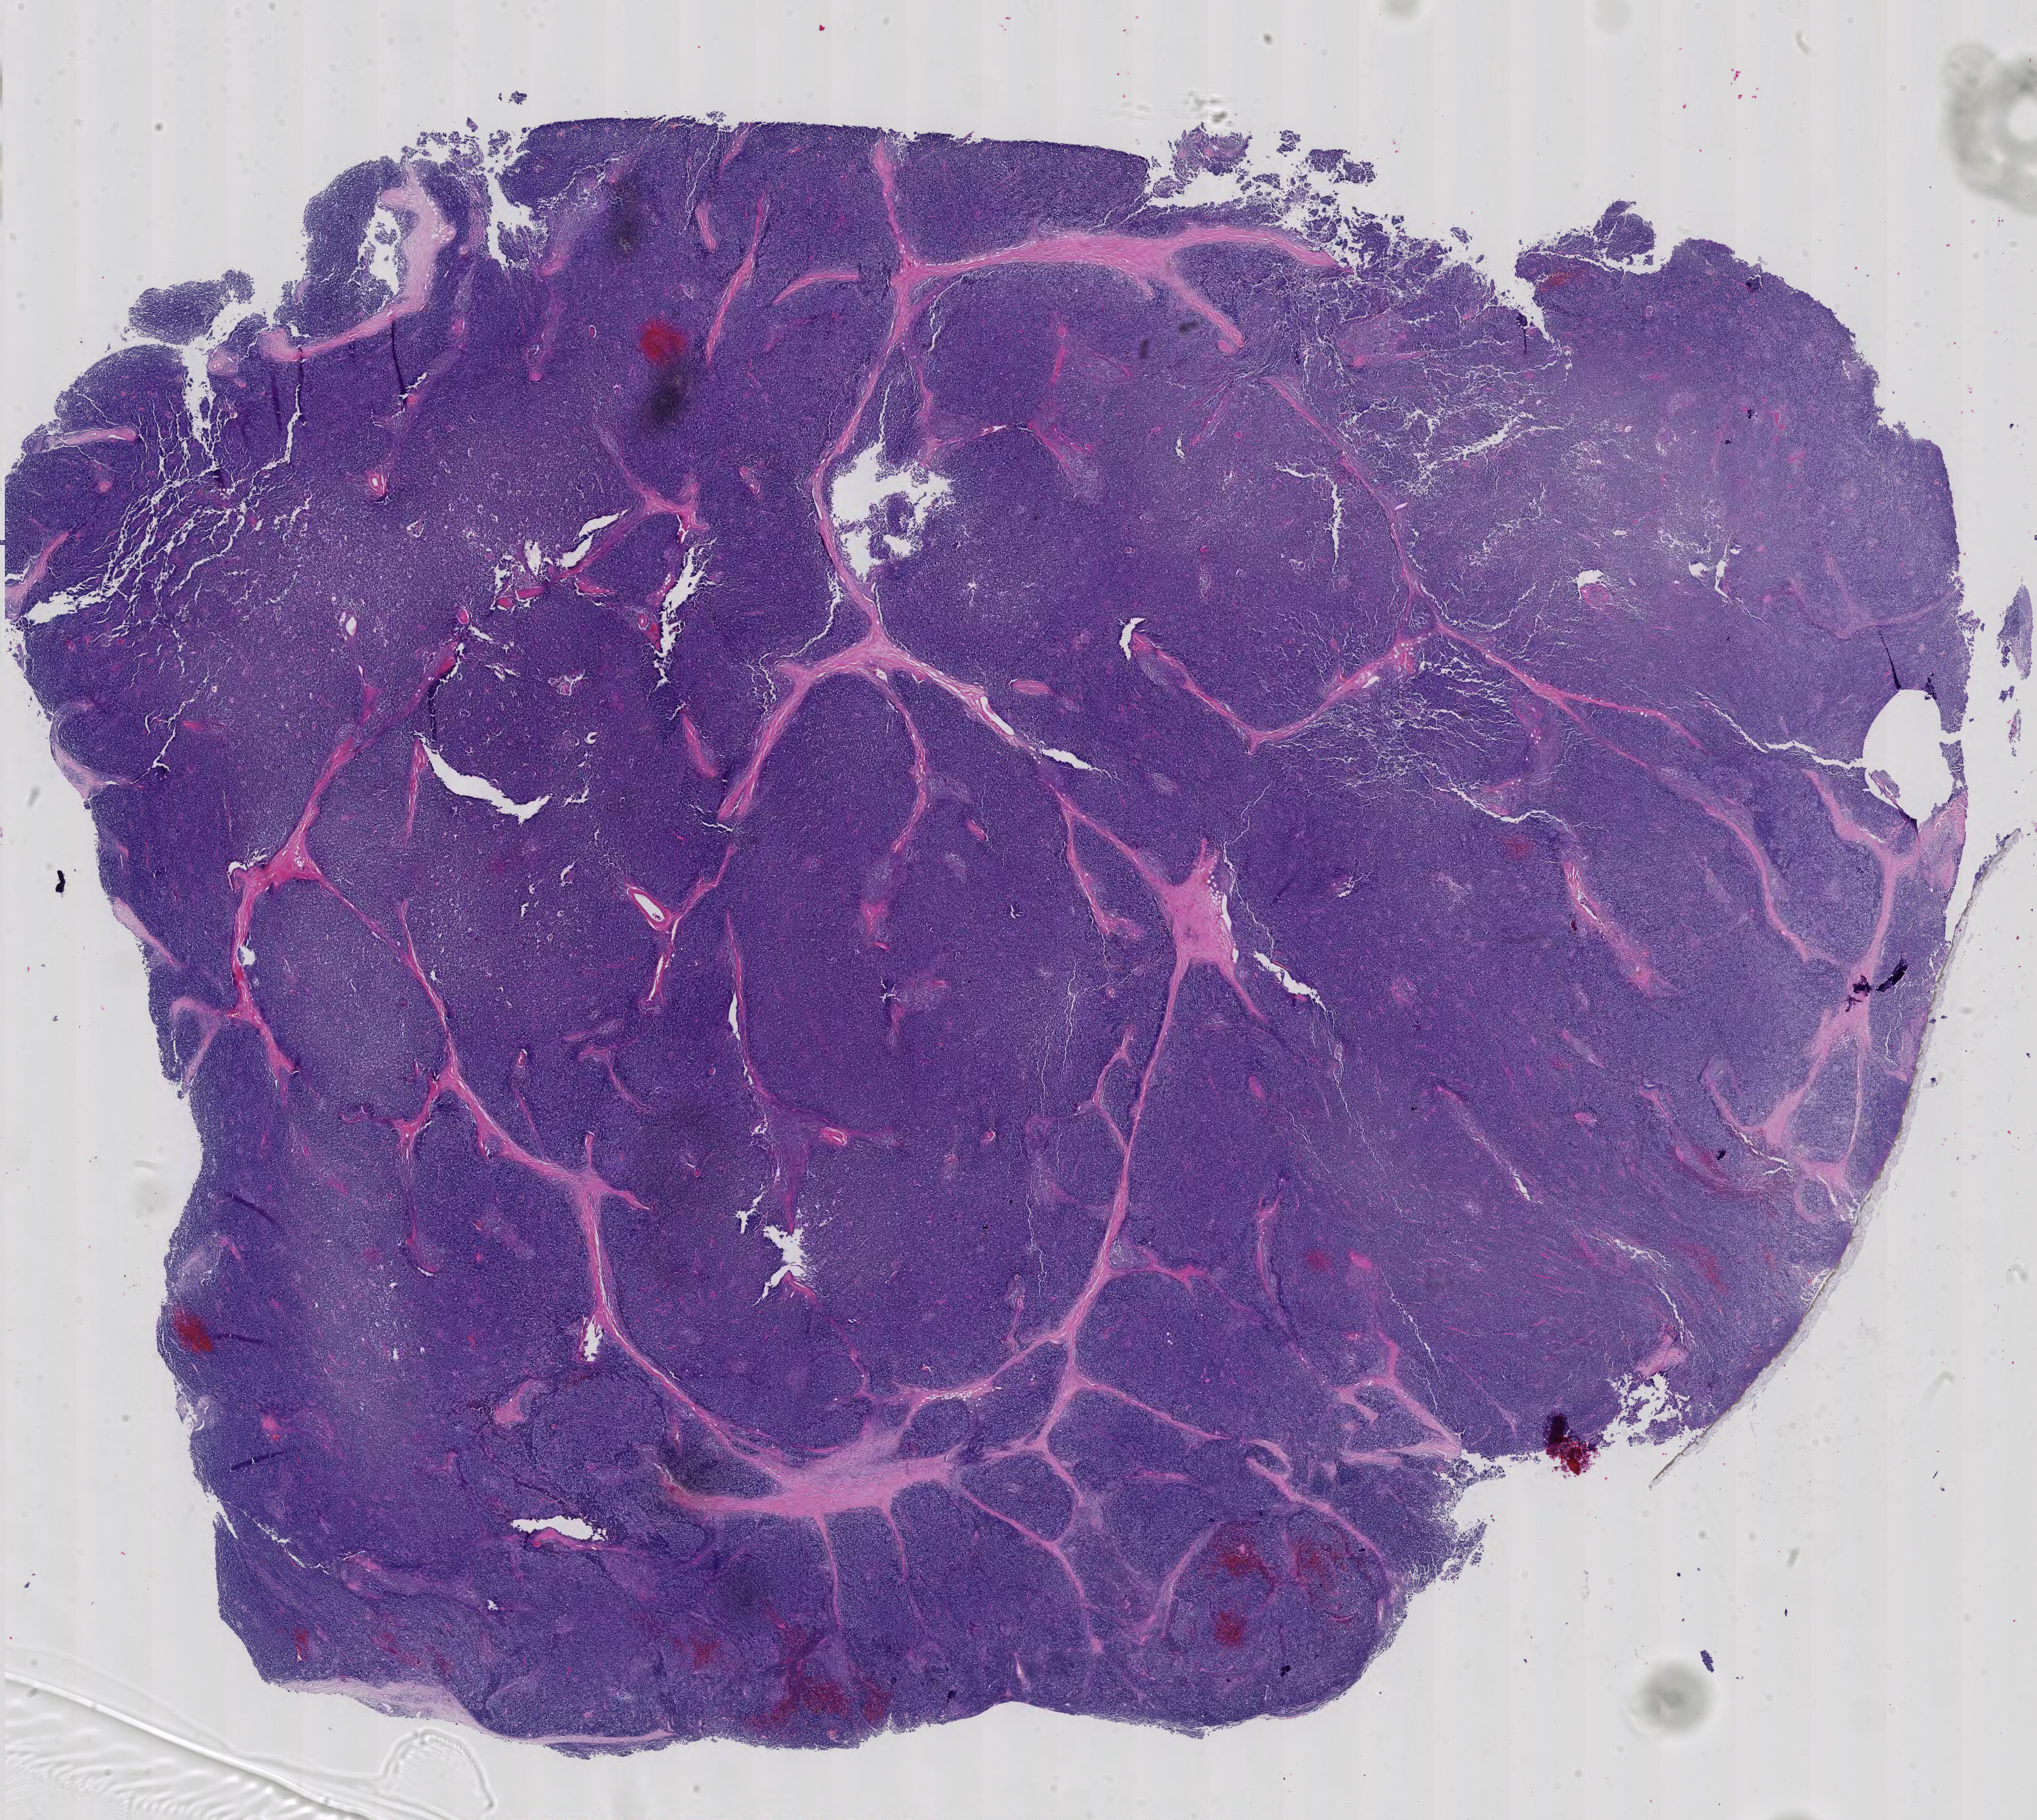
Digitized H&E-stained tissue section (whole slide) — low-resolution overview of the scanned area, about 24.4 x 21.8 mm (from a 40x scan); formalin-fixed paraffin-embedded (FFPE) diagnostic section; thymus, primary tumour sample. Patient: male, age at initial diagnosis 38 years.
* pathologic diagnosis: Thymoma, type B2, malignant (anterior mediastinum)